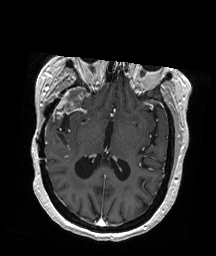
Brain MRI from a brain-tumour surgery series, one axial slice. Position 102 of 192 along the scan axis. T1-weighted post-contrast. 216 × 256 image matrix, field of view 211 × 250 mm. Case-level facts recorded for this patient, not image findings: histopathology: Glioblastoma; WHO grade: 4.
Structures marked on this image (expert manual segmentation):
- tumour: bounding box [x1, y1, x2, y2] px = [56, 87, 87, 114]